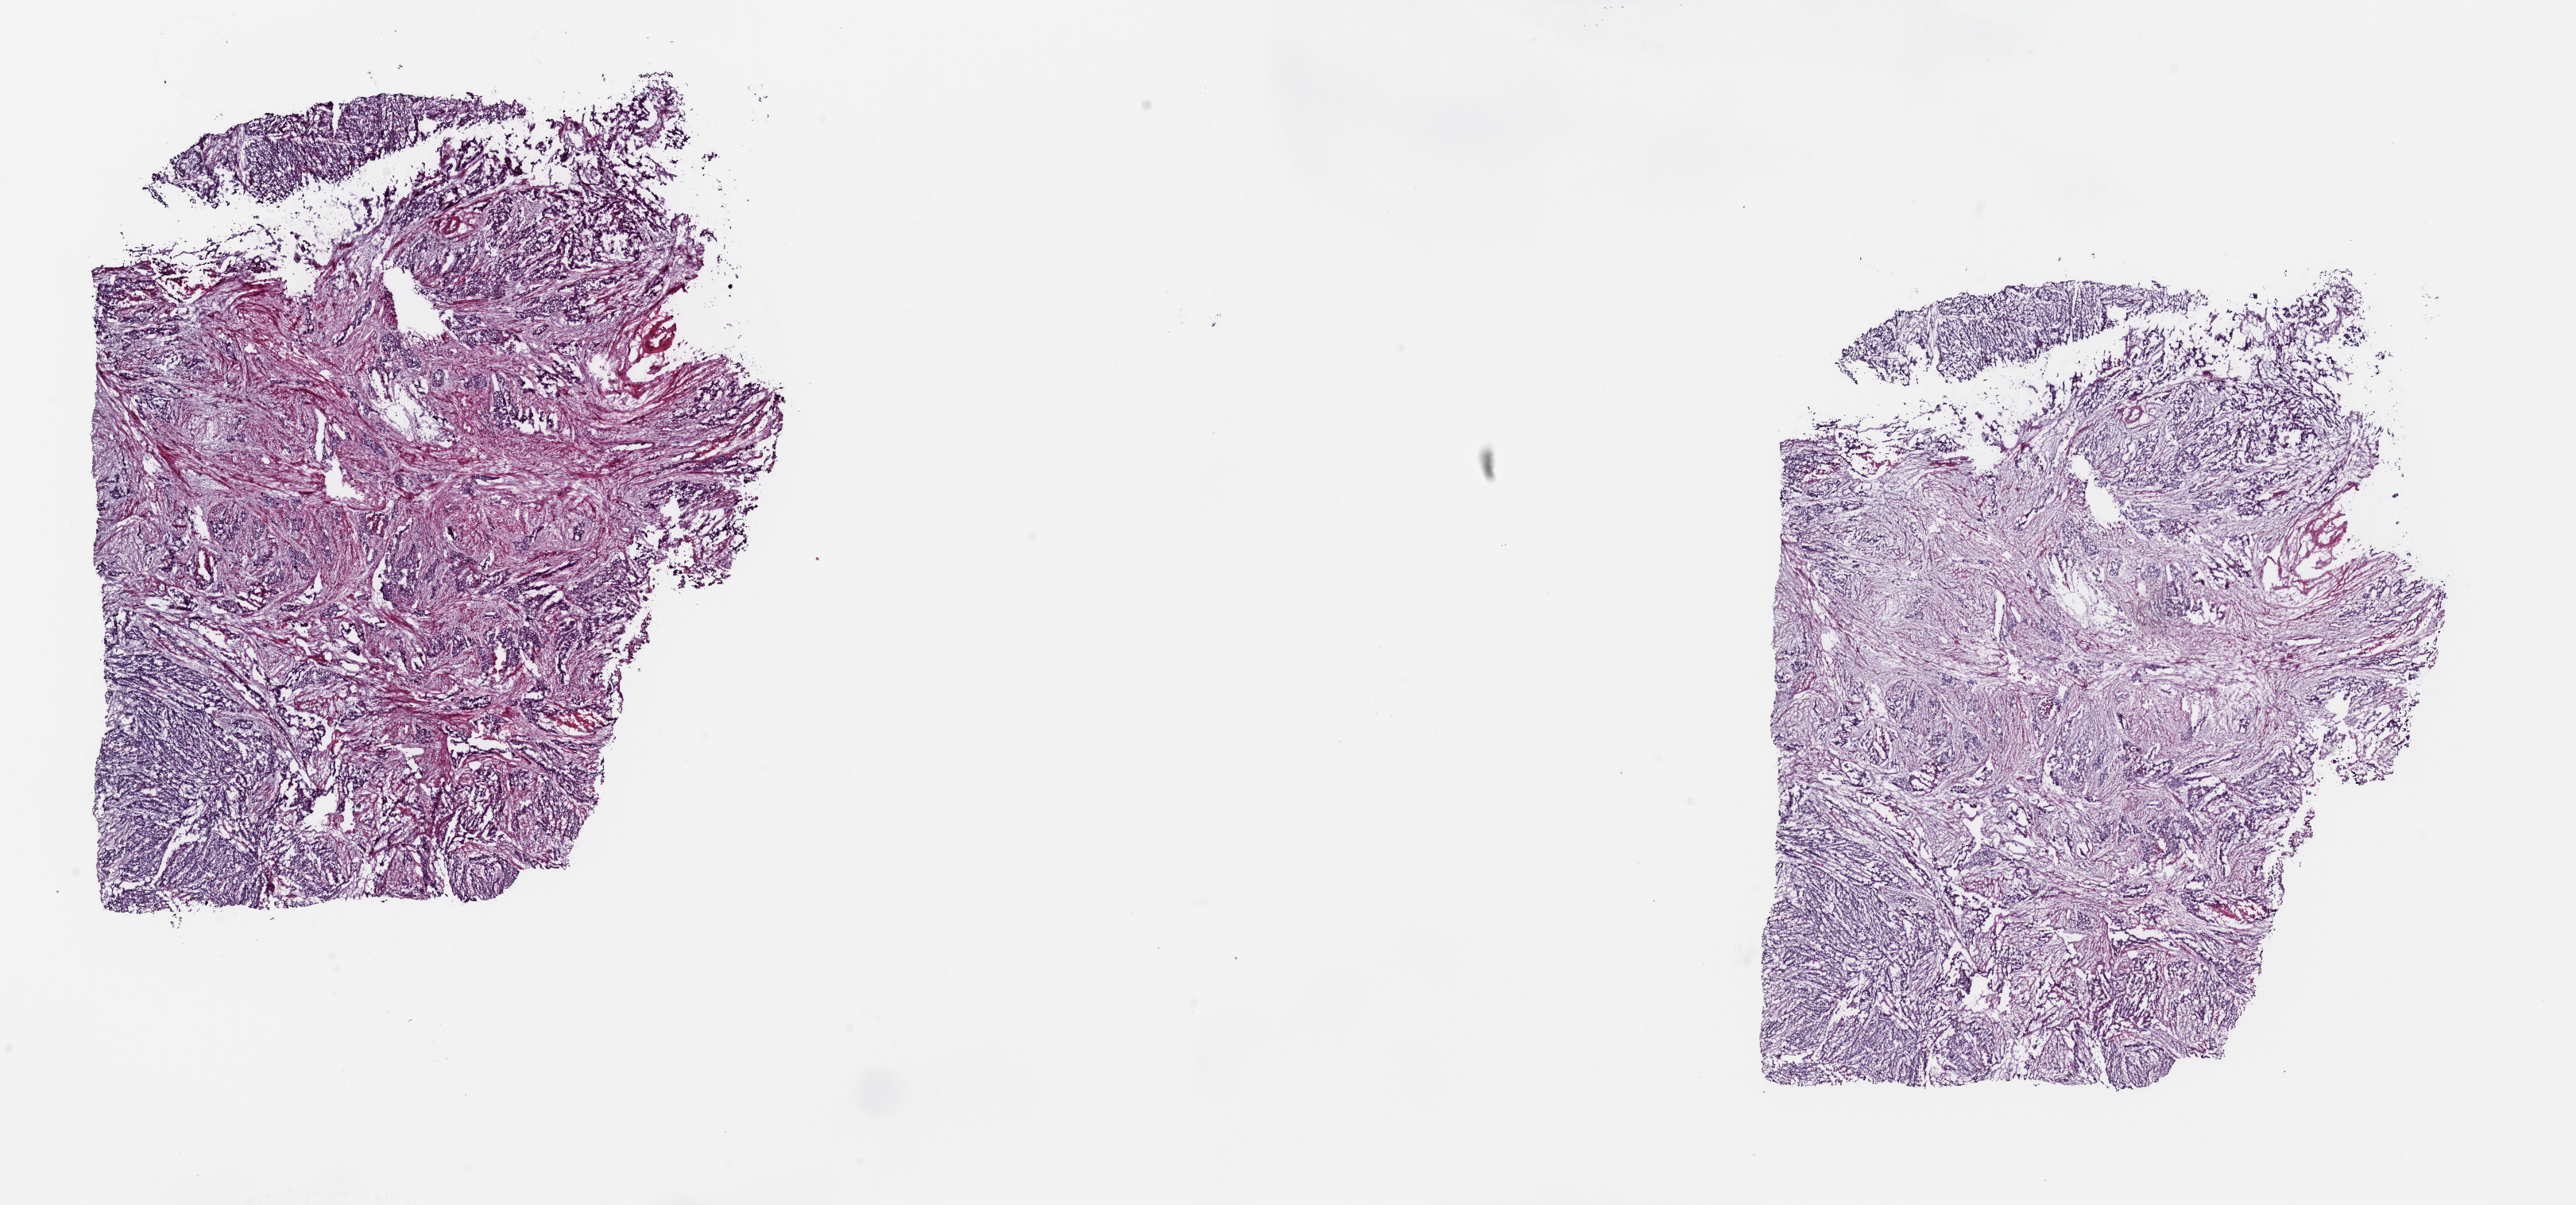
Whole-slide histology image, H&E — a low-resolution overview of the entire scanned area, about 25.6 x 12.0 mm. Frozen section. Primary tumour sample from the uterus. Female, age 82 years at initial diagnosis. Histologic grade: G3 (poorly differentiated). Composition of this section per pathologist review: tumour cells 80%, tumour nuclei 70%, normal cells 15%, stromal cells 0%, necrosis 5%. Inflammatory infiltration, as recorded: lymphocyte infiltration 2%, monocyte infiltration 0%, neutrophil infiltration 0%.
* pathologic diagnosis: Serous cystadenocarcinoma, NOS (endometrium)
* FIGO stage: II